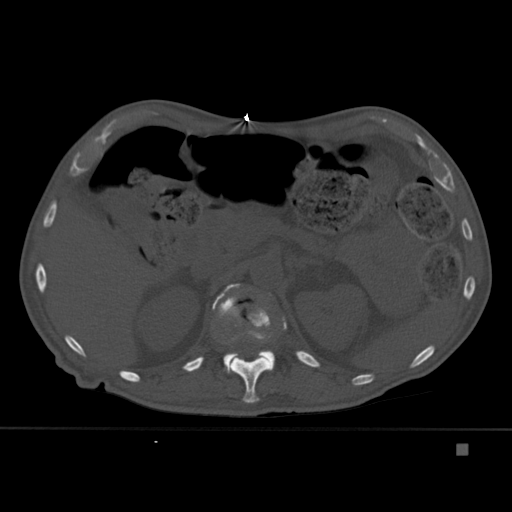
CT including the spine, one axial slice; slice 194 of 451 in the series (ordered by position); bone window (W 1800 / L 400 HU); 1.5 mm slice thickness; 512 × 512 image matrix, field of view 378 × 378 mm. Male patient, age 75 years. Case-level facts recorded for this patient, not image findings: primary cancer: prostate.
Annotated regions visible in this slice (semi-automatic segmentation, software-assisted and operator-edited):
- L1 vertebra: bounding box [x1, y1, x2, y2] px = [212, 284, 275, 374]
- T12 vertebra: [230, 308, 287, 403]